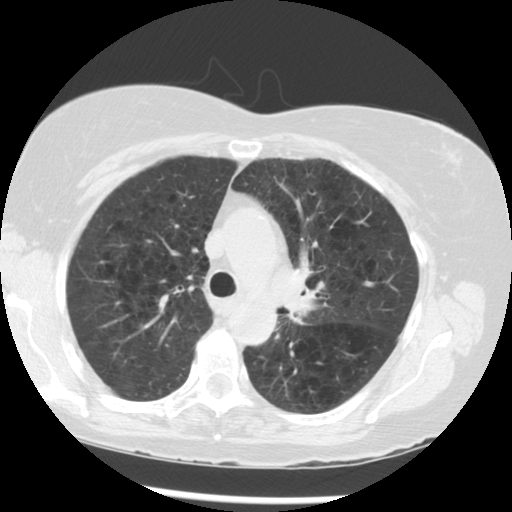
Chest CT (low-dose screening protocol), one axial image, third screening round (two years after baseline), lung window (W 1500 / L -600 HU), standard (soft-tissue) reconstruction kernel (STANDARD), 120 kVp, slice 205 of 283 in the series, 512 × 512 image matrix, field of view 330 × 330 mm. Female, age 70 years at enrolment. Current smoker at enrolment.
Lesion marked by an expert reader, bounding box (x1, y1, x2, y2) in pixels: (272, 258, 365, 350). Reader record for this screening exam (exam-level; its link to the box is not recorded): non-calcified nodule or mass ≥4 mm, left upper lobe, 32 × 26 mm, spiculated (stellate) margins, soft tissue attenuation, pre-existing on the prior screen: yes; interval growth: yes. Official screen result: positive, other. Participant outcome: lung cancer diagnosed 24 days after this screen — neoplasm, malignant, left upper lobe, stage IIIB (AJCC 6th edition), 40 mm at pathology.